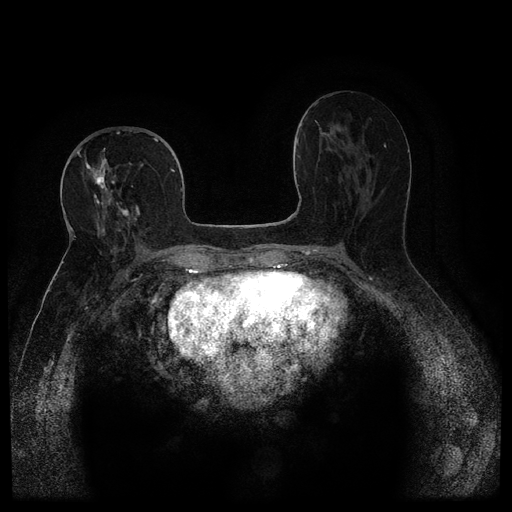
Breast MRI (dynamic contrast-enhanced, multi-phase), one axial slice; slice 54 of 116 in the series (ordered by position); dynamic contrast-enhanced series, time point 2 of 5 at this slice position (early post-contrast); 1.5 T; TE 2.6 ms, TR 5.4 ms; 2 mm slice thickness; 512 × 512 image matrix, field of view 340 × 340 mm. Patient: female, 68 years.
Annotated regions visible in this slice (semi-automatic segmentation, software-assisted and operator-edited):
- breast lesion (labelled 'tumour' in the annotation; benign lesions carry a separate 'benign' label): bounding box [x1, y1, x2, y2] px = [84, 147, 119, 218]